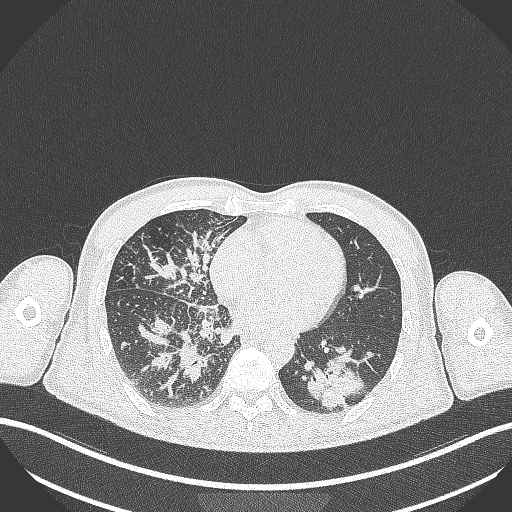
Chest CT, one axial slice. Position 123 of 348 along the scan axis. 120 kVp. Lung window (W 1500 / L -600 HU). 1 mm slice thickness. 512 × 512 image matrix, field of view 400 × 400 mm. Male patient, age 49 years. Case-level facts recorded for this patient, not image findings: clinical TNM (as recorded): T2b N1 M0.
Annotated regions visible in this slice (rectangle marked by the reading radiologist):
- lung tumour (recorded histology: adenocarcinoma): bounding box <303,355,371,414> (left, top, right, bottom; pixels)